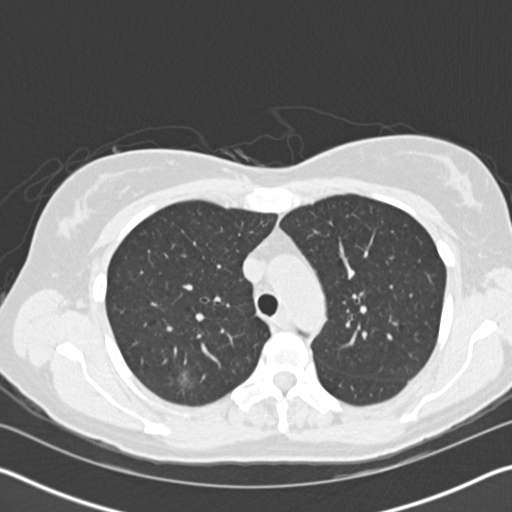
Axial slice from a low-dose chest CT screening exam, baseline annual screen, lung window (W 1500 / L -600 HU), 2 mm slice thickness, standard (soft-tissue) reconstruction kernel (B30f), 120 kVp, 512 × 512 image matrix. Female, age 58 years at enrolment. Current smoker at enrolment.
Expert reader's lesion annotation, bounding box <156,357,210,406> (left, top, right, bottom; pixels). The screening reader recorded 3 non-calcified nodules or masses ≥4 mm on this exam (right upper lobe, left upper lobe, left upper lobe); which of them this box marks is not recorded. Official screen result: positive, change unspecified: nodule(s) >= 4 mm or enlarging nodule(s), mass(es), or other non-specific abnormalities suspicious for lung cancer.